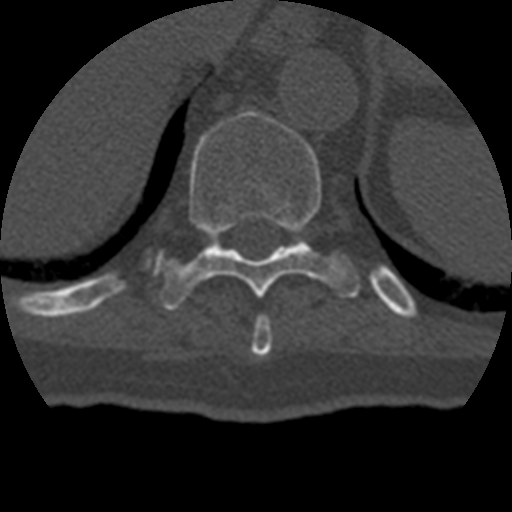
CT including the spine, one axial slice. Slice 218 of 399 in the series (ordered by position). 120 kVp. Bone window (W 1800 / L 400 HU). 1.25 mm slice thickness. 512 × 512 image matrix. Patient age 69 years. Case-level facts recorded for this patient, not image findings: primary cancer: prostate.
Annotated regions visible in this slice (semi-automatically segmented with operator editing):
- T10 vertebra: box from (x=161, y=111) to (x=360, y=311) px
- T9 vertebra: (x=252, y=315)–(x=273, y=357)